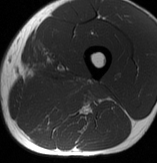
MRI of an extremity soft-tissue mass, one axial slice. Position 28 of 70 along the scan axis. MR volume resampled by the dataset authors to the PET/CT grid (not the native acquisition matrix). 3.27 mm slice thickness. 157 × 163 image matrix, field of view 153 × 159 mm. Male patient. Case-level facts recorded for this patient, not image findings: histological type: extraskeletal osteosarcoma; grade: high; site of the primary tumour: left adductur.
Structures marked on this image (expert contour drawn on MRI and transferred to this co-registered scan by the dataset authors):
- gross tumour volume (mass): box from (x=24, y=71) to (x=112, y=130) px